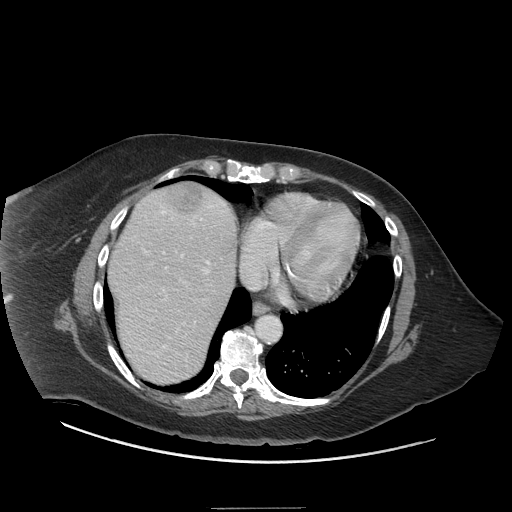
Contrast-enhanced abdominal CT (liver protocol), one axial slice; slice 62 of 81 in the series (ordered by position); reconstruction kernel STANDARD; 140 kVp; soft-tissue window (W 400 / L 40 HU); 512 × 512 image matrix, field of view 440 × 440 mm. Case-level facts recorded for this patient, not image findings: diagnosis: hepatocellular carcinoma (patient treated with transarterial chemoembolisation; whether this scan precedes or follows treatment is not stated here); TNM stage (as recorded): Stage-II; Child-Pugh class: A; tumour differentiation: moderately differentiated; tumour nodularity: multinodular.
Outlined on this slice (semi-automatic segmentation, software-assisted and operator-edited):
- abdominal aorta: bounding box (x1, y1, x2, y2) in pixels: (256, 316, 280, 342)
- liver parenchyma outside the tumour (the mass and vessels are separate outlines, so this box may not span the whole liver): (108, 182, 236, 384)
- mass: (169, 184, 204, 212)
- liver vessels: (127, 199, 226, 375)